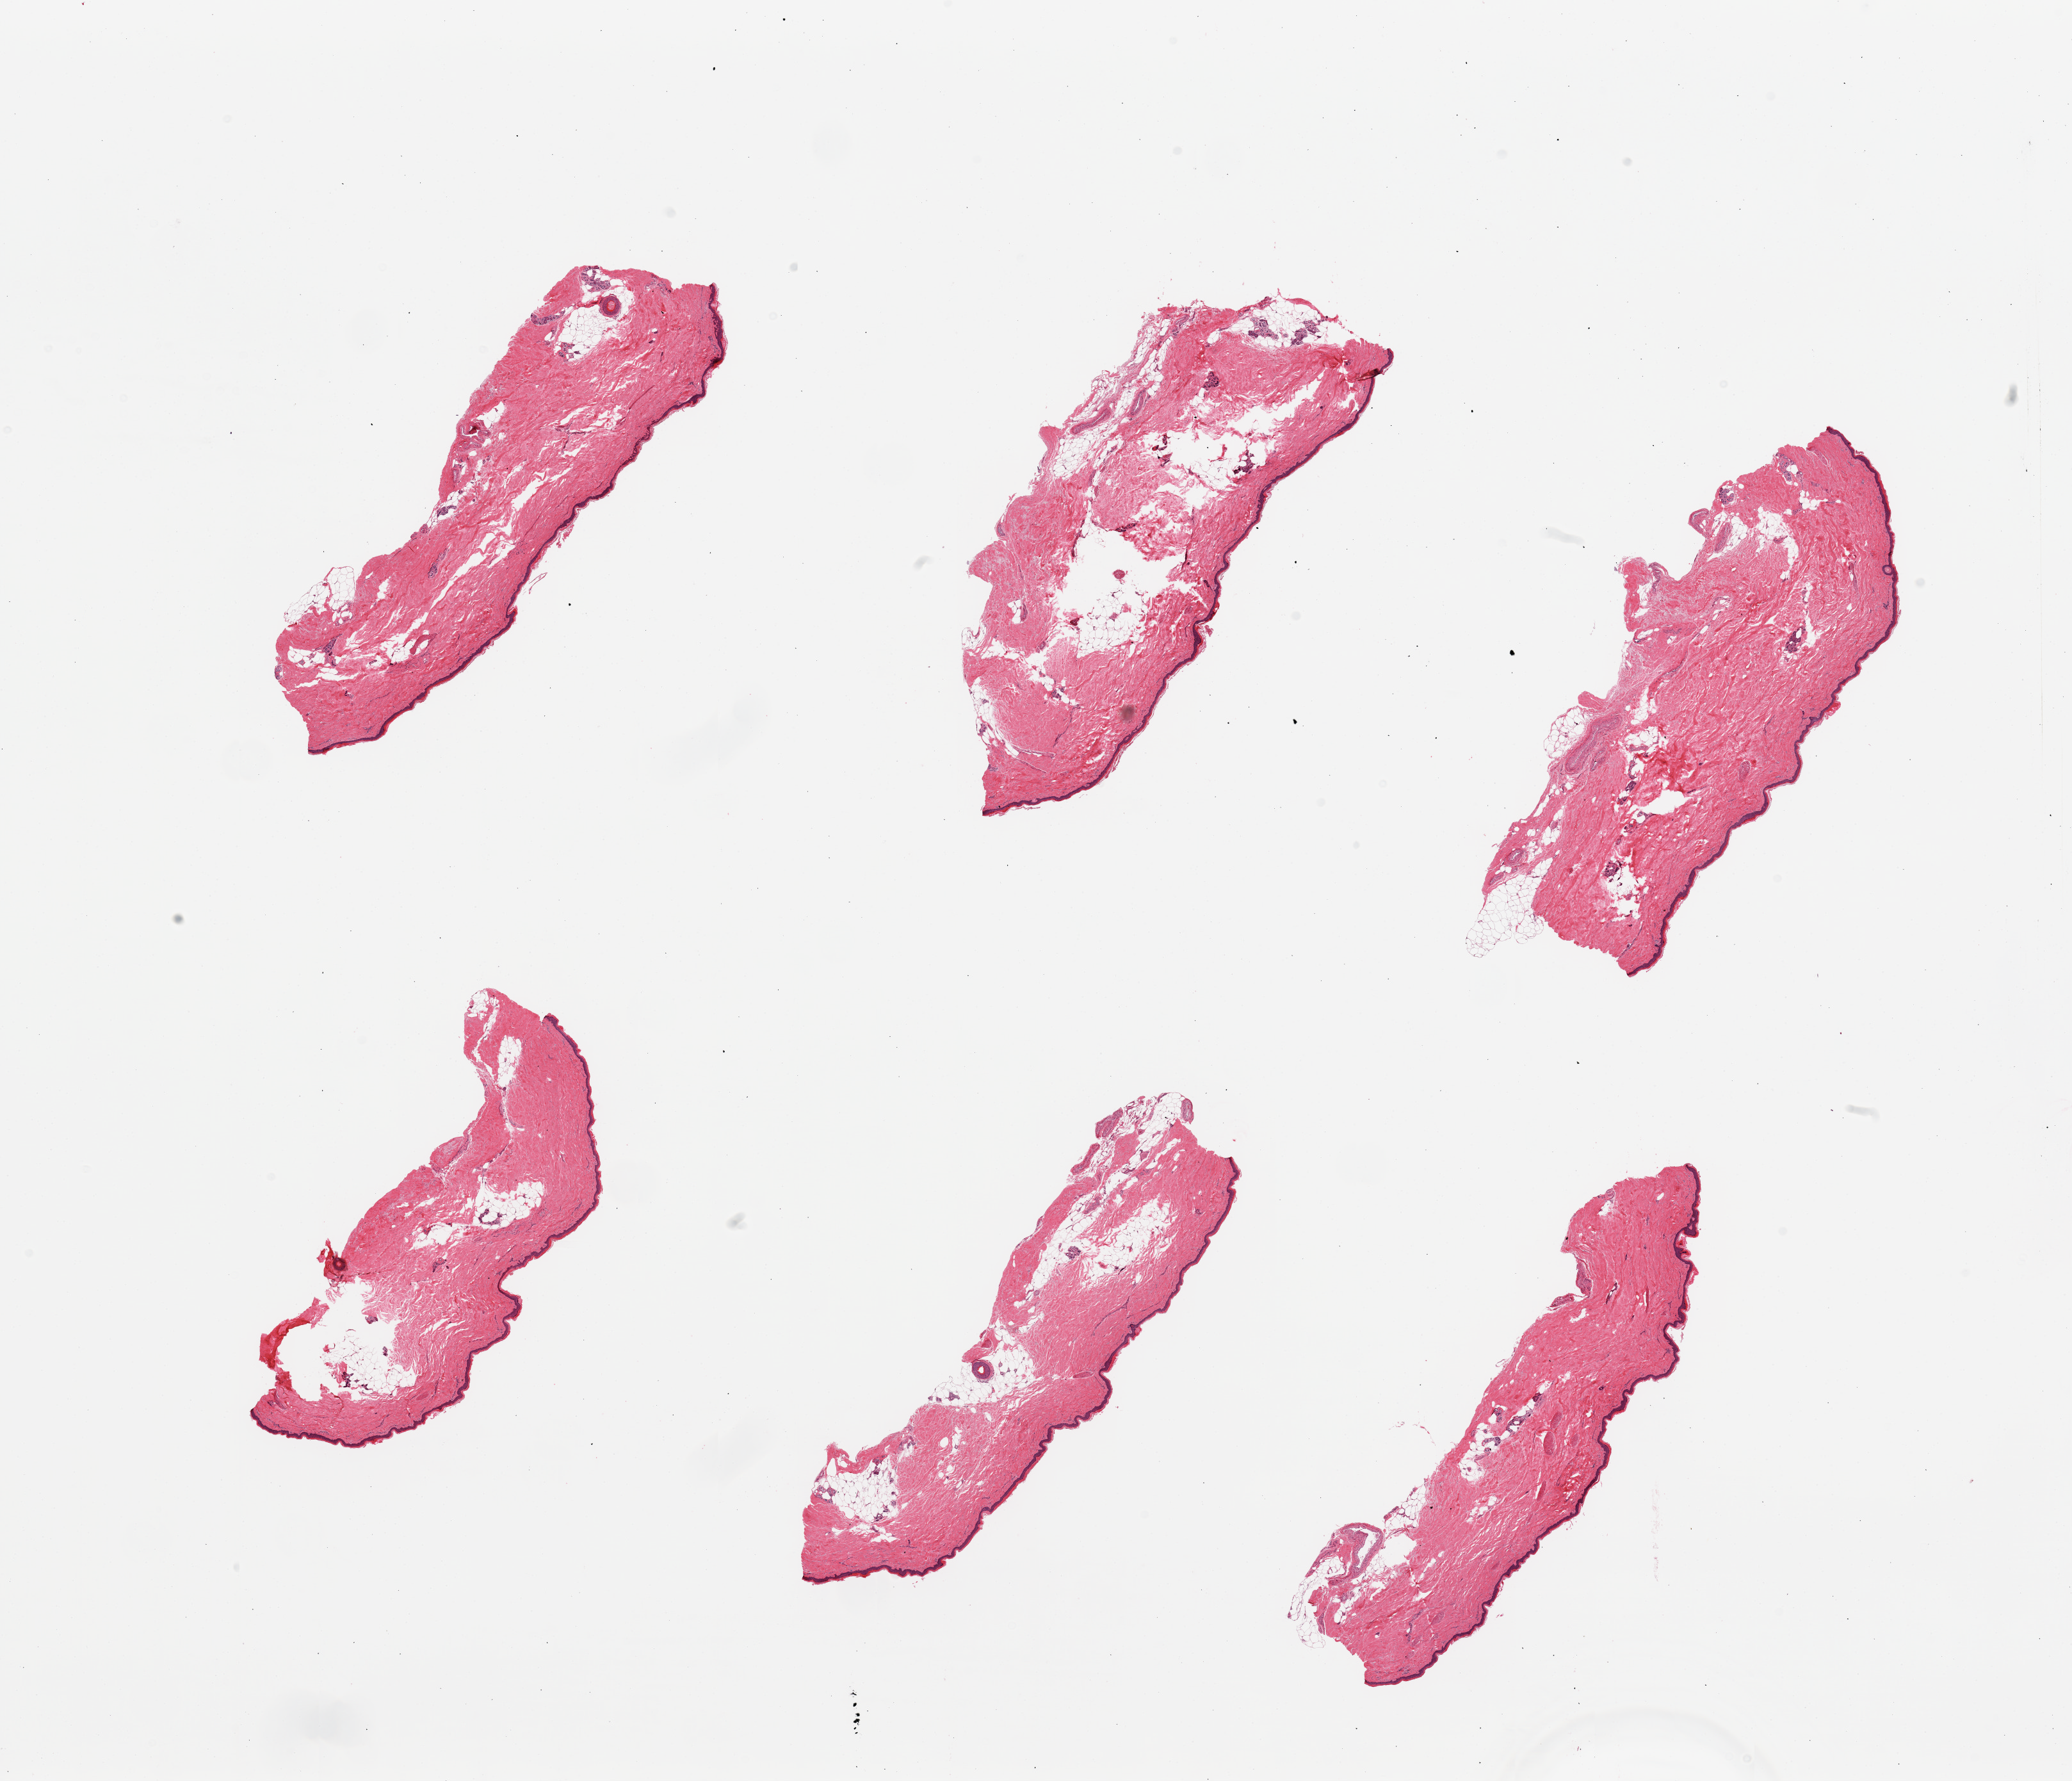
Whole-slide image, hematoxylin and eosin (H&E) stain — shown as a low-resolution overview of the whole scanned area (about 25.6 x 22.0 mm, slide scanned at 20x); PAXgene-fixed paraffin-embedded (PFPE) section; sampled site (target tissue): skin of lower leg; donor tissue sample. Female donor.
Reviewer comment on this tissue sample: 6 pieces; well trimmed deep surface; up to 30% intradermal fat.